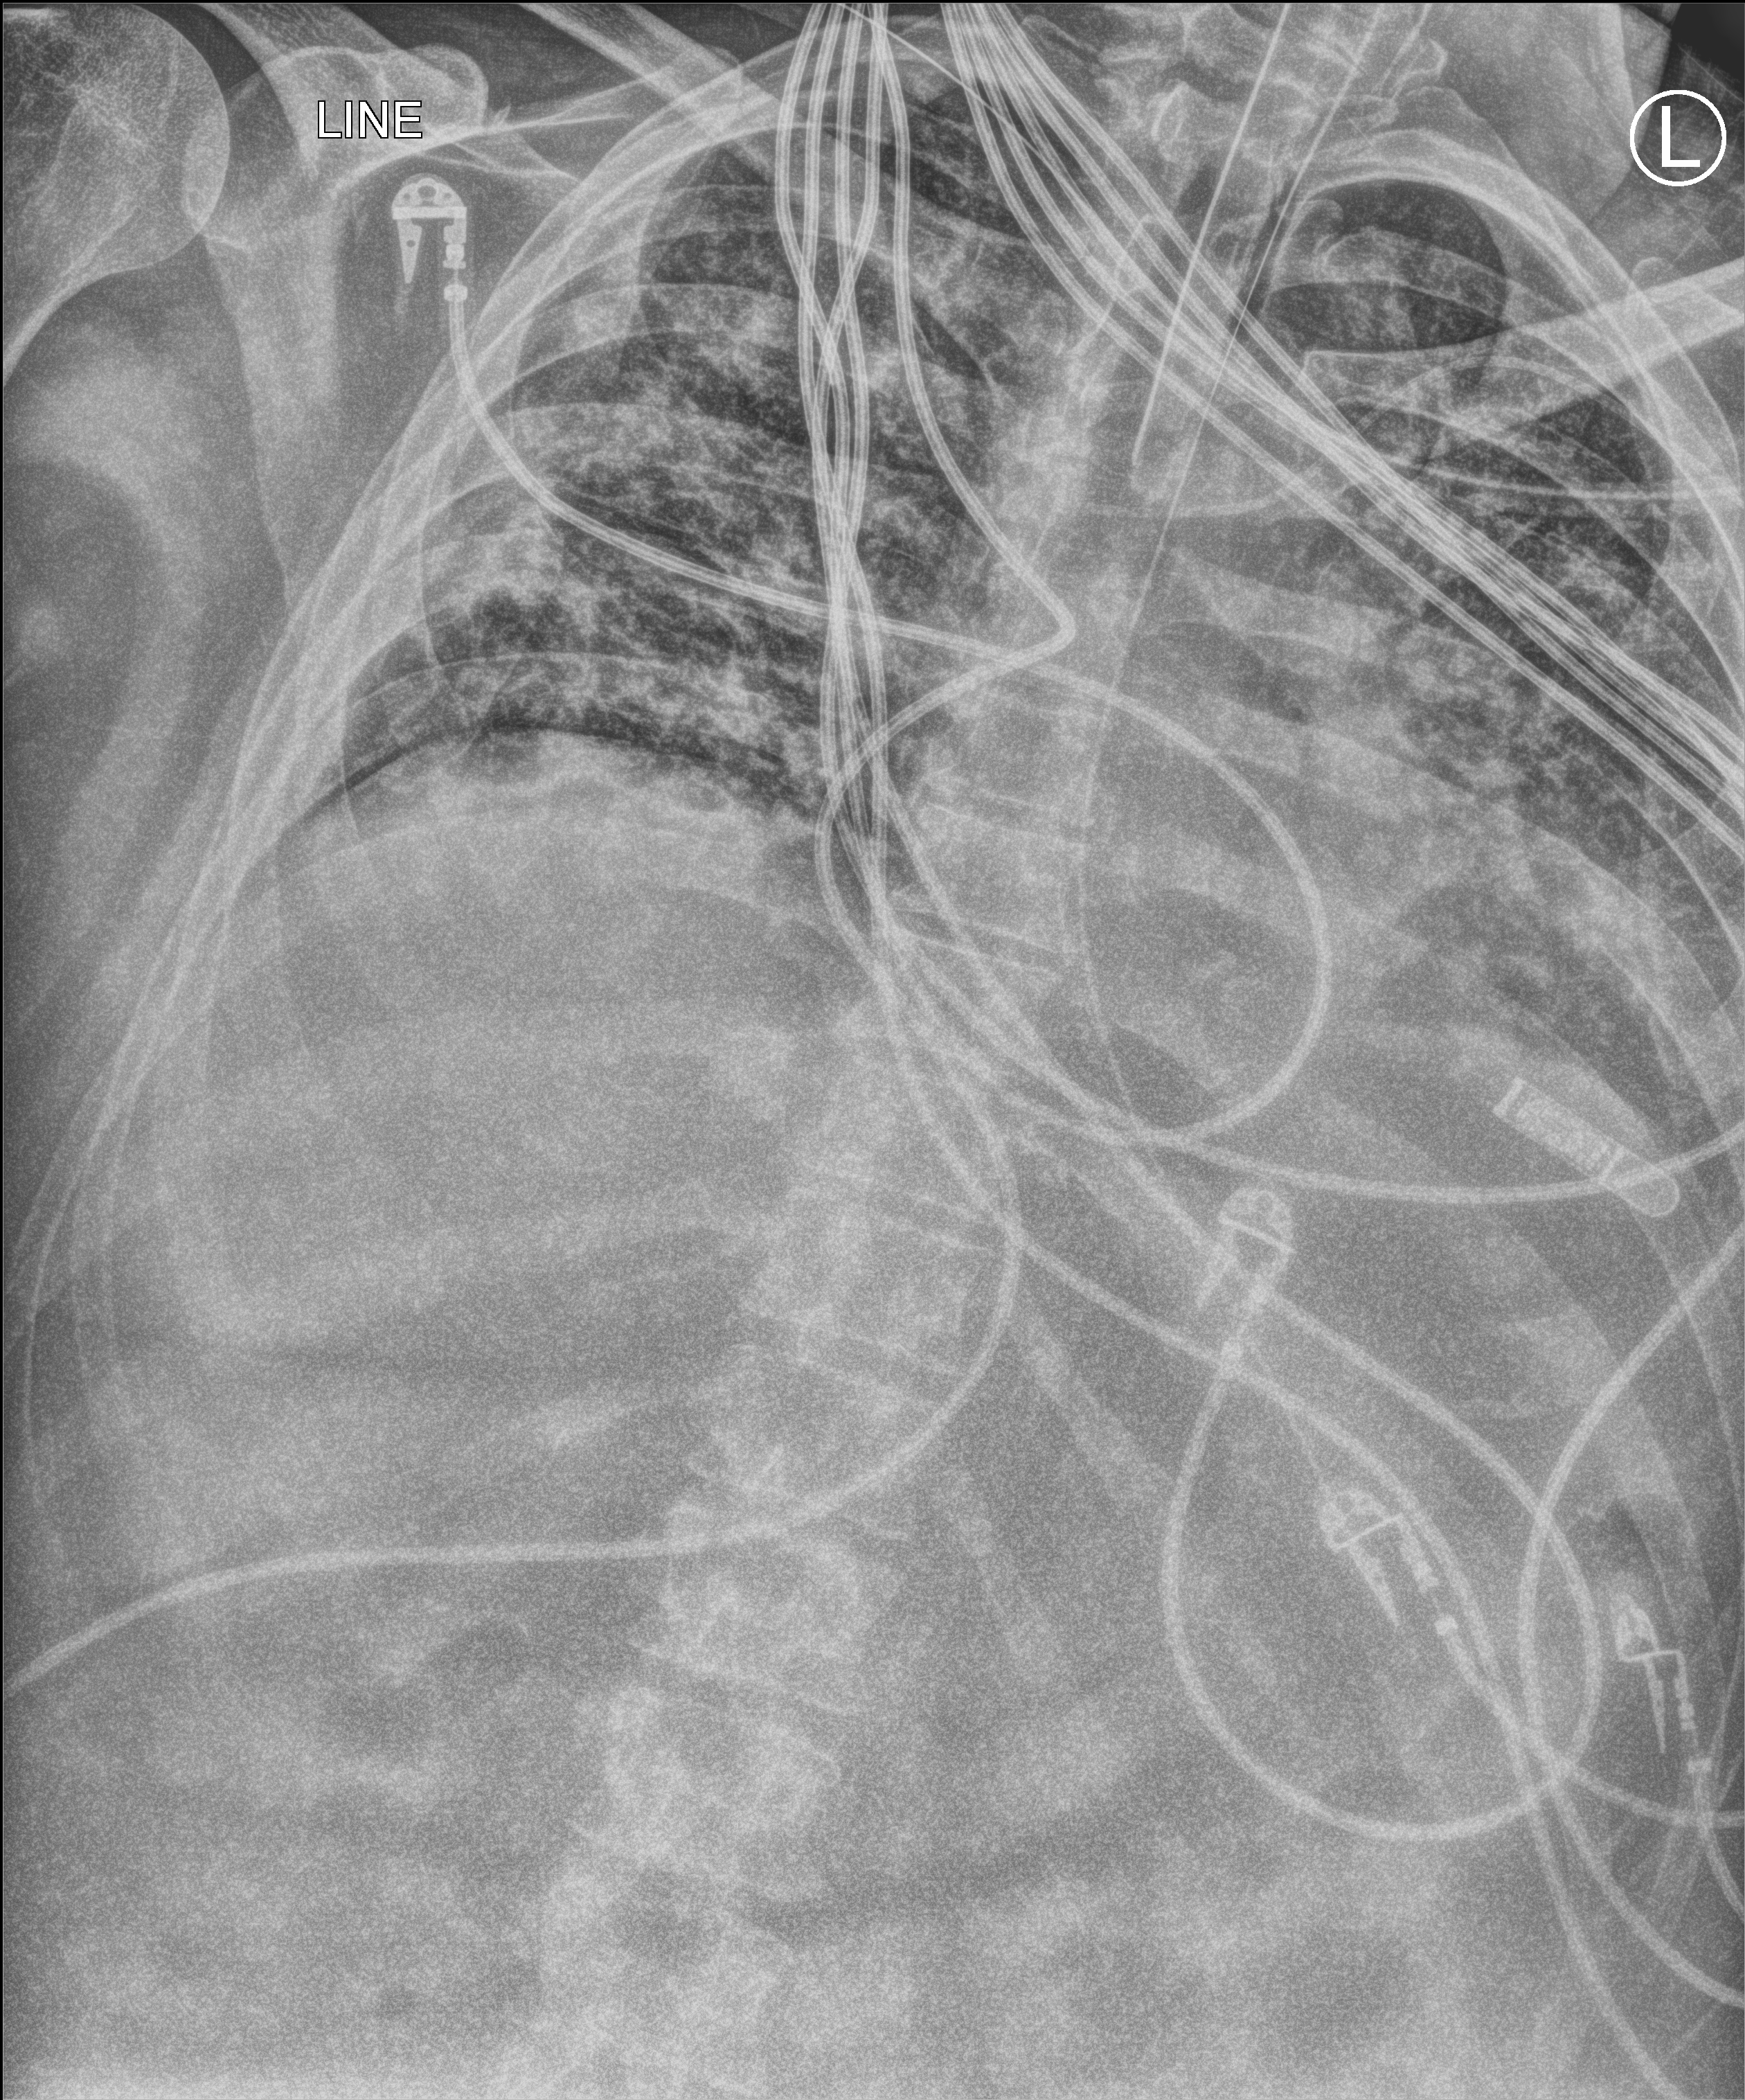
Chest X-ray (portable), anteroposterior (AP) projection. Patient hospitalised with COVID-19; male, aged 18–59 years.
Hospital-stay facts (about this admission, not read from this image; timing relative to this image not recorded): mechanically ventilated during this hospital stay: yes; admitted to intensive care during this hospital stay: yes.